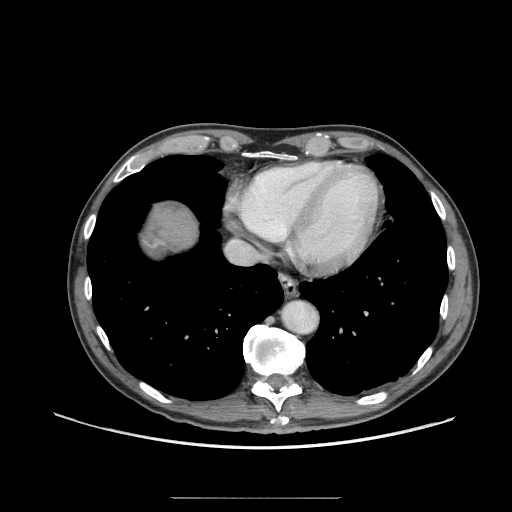
Contrast-enhanced abdominal CT (liver protocol), one axial slice. Position 66 of 71 along the scan axis. 140 kVp. Soft-tissue window (W 400 / L 40 HU). 2.5 mm slice thickness. 512 × 512 image matrix. Case-level facts recorded for this patient, not image findings: diagnosis: hepatocellular carcinoma (patient treated with transarterial chemoembolisation; whether this scan precedes or follows treatment is not stated here); TNM stage (as recorded): Stage-I; Child-Pugh class: A; tumour differentiation: well differentiated; tumour nodularity: uninodular.
Structures marked on this image (semi-automatic segmentation, software-assisted and operator-edited):
- abdominal aorta: bounding box <282,301,317,333> (left, top, right, bottom; pixels)
- liver parenchyma outside the tumour (the mass and vessels are separate outlines, so this box may not span the whole liver): <148,210,194,248>